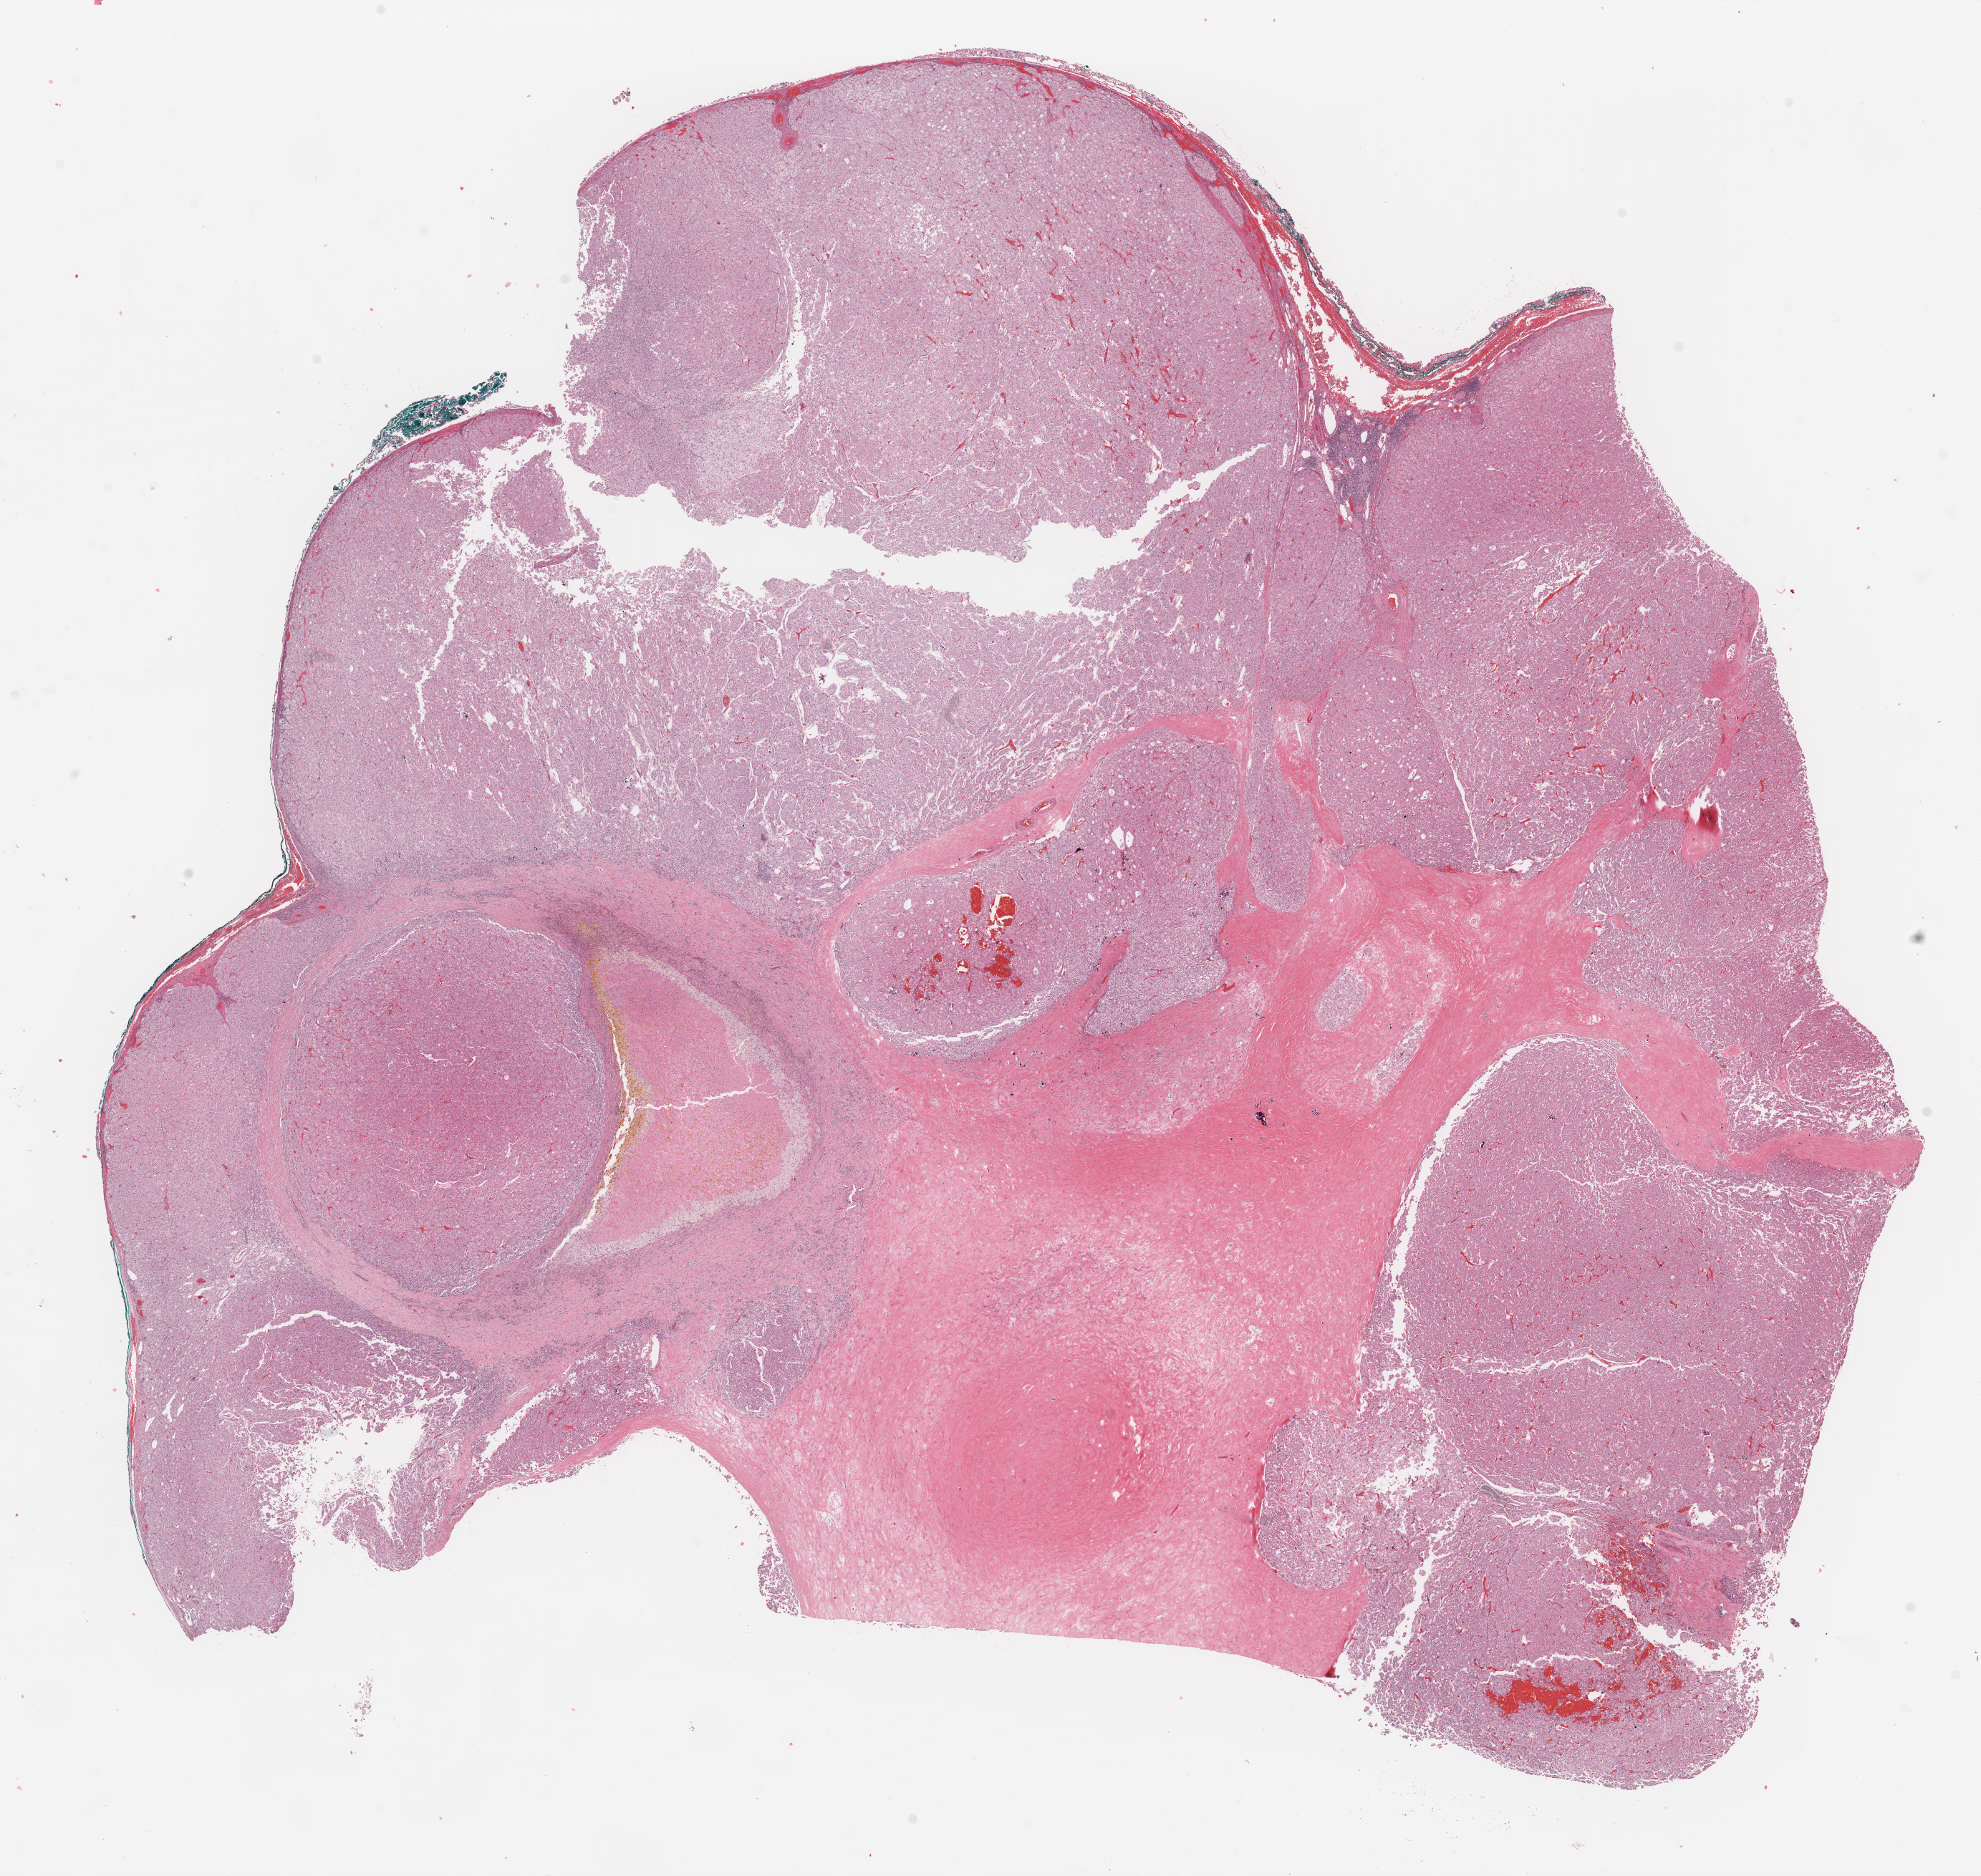
Digitized H&E tissue section (whole slide) — low-resolution overview of the scanned area, about 21.9 x 20.7 mm (acquisition: 40x scan); formalin-fixed paraffin-embedded (FFPE) diagnostic section; kidney, primary tumour sample. Male patient; age at initial diagnosis 31 years. Pathologist review of this section (percent, as recorded): tumour cells 80%, tumour nuclei 80%, normal cells 0%, stromal cells 20%, necrosis 0%. Inflammatory infiltration, as recorded: lymphocyte infiltration 0%, monocyte infiltration 0%, neutrophil infiltration 0%.
AJCC pathologic stage: III (6th edition). Laterality: left. Diagnosis: Renal cell carcinoma, chromophobe type.